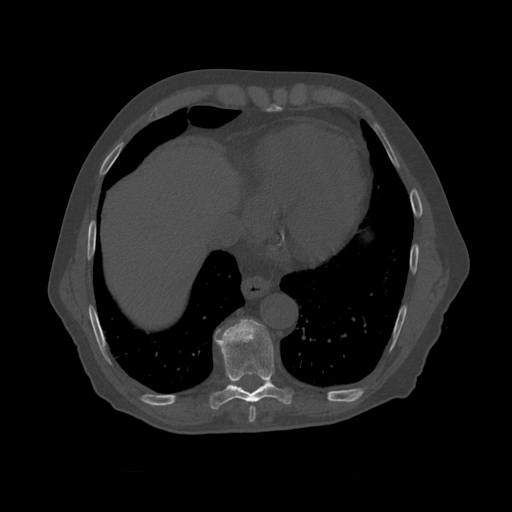
CT including the spine, one axial slice; position 445 of 450 along the scan axis; reconstruction kernel STANDARD; 120 kVp; bone window (W 1800 / L 400 HU); 1.25 mm slice thickness; 512 × 512 image matrix, field of view 405 × 405 mm. Patient age 75 years. From the clinical record (not read from this slice): primary cancer: prostate.
Structures marked on this image (semi-automatic segmentation, software-assisted and operator-edited):
- T8 vertebra: bounding box <215,319,293,410> (left, top, right, bottom; pixels)